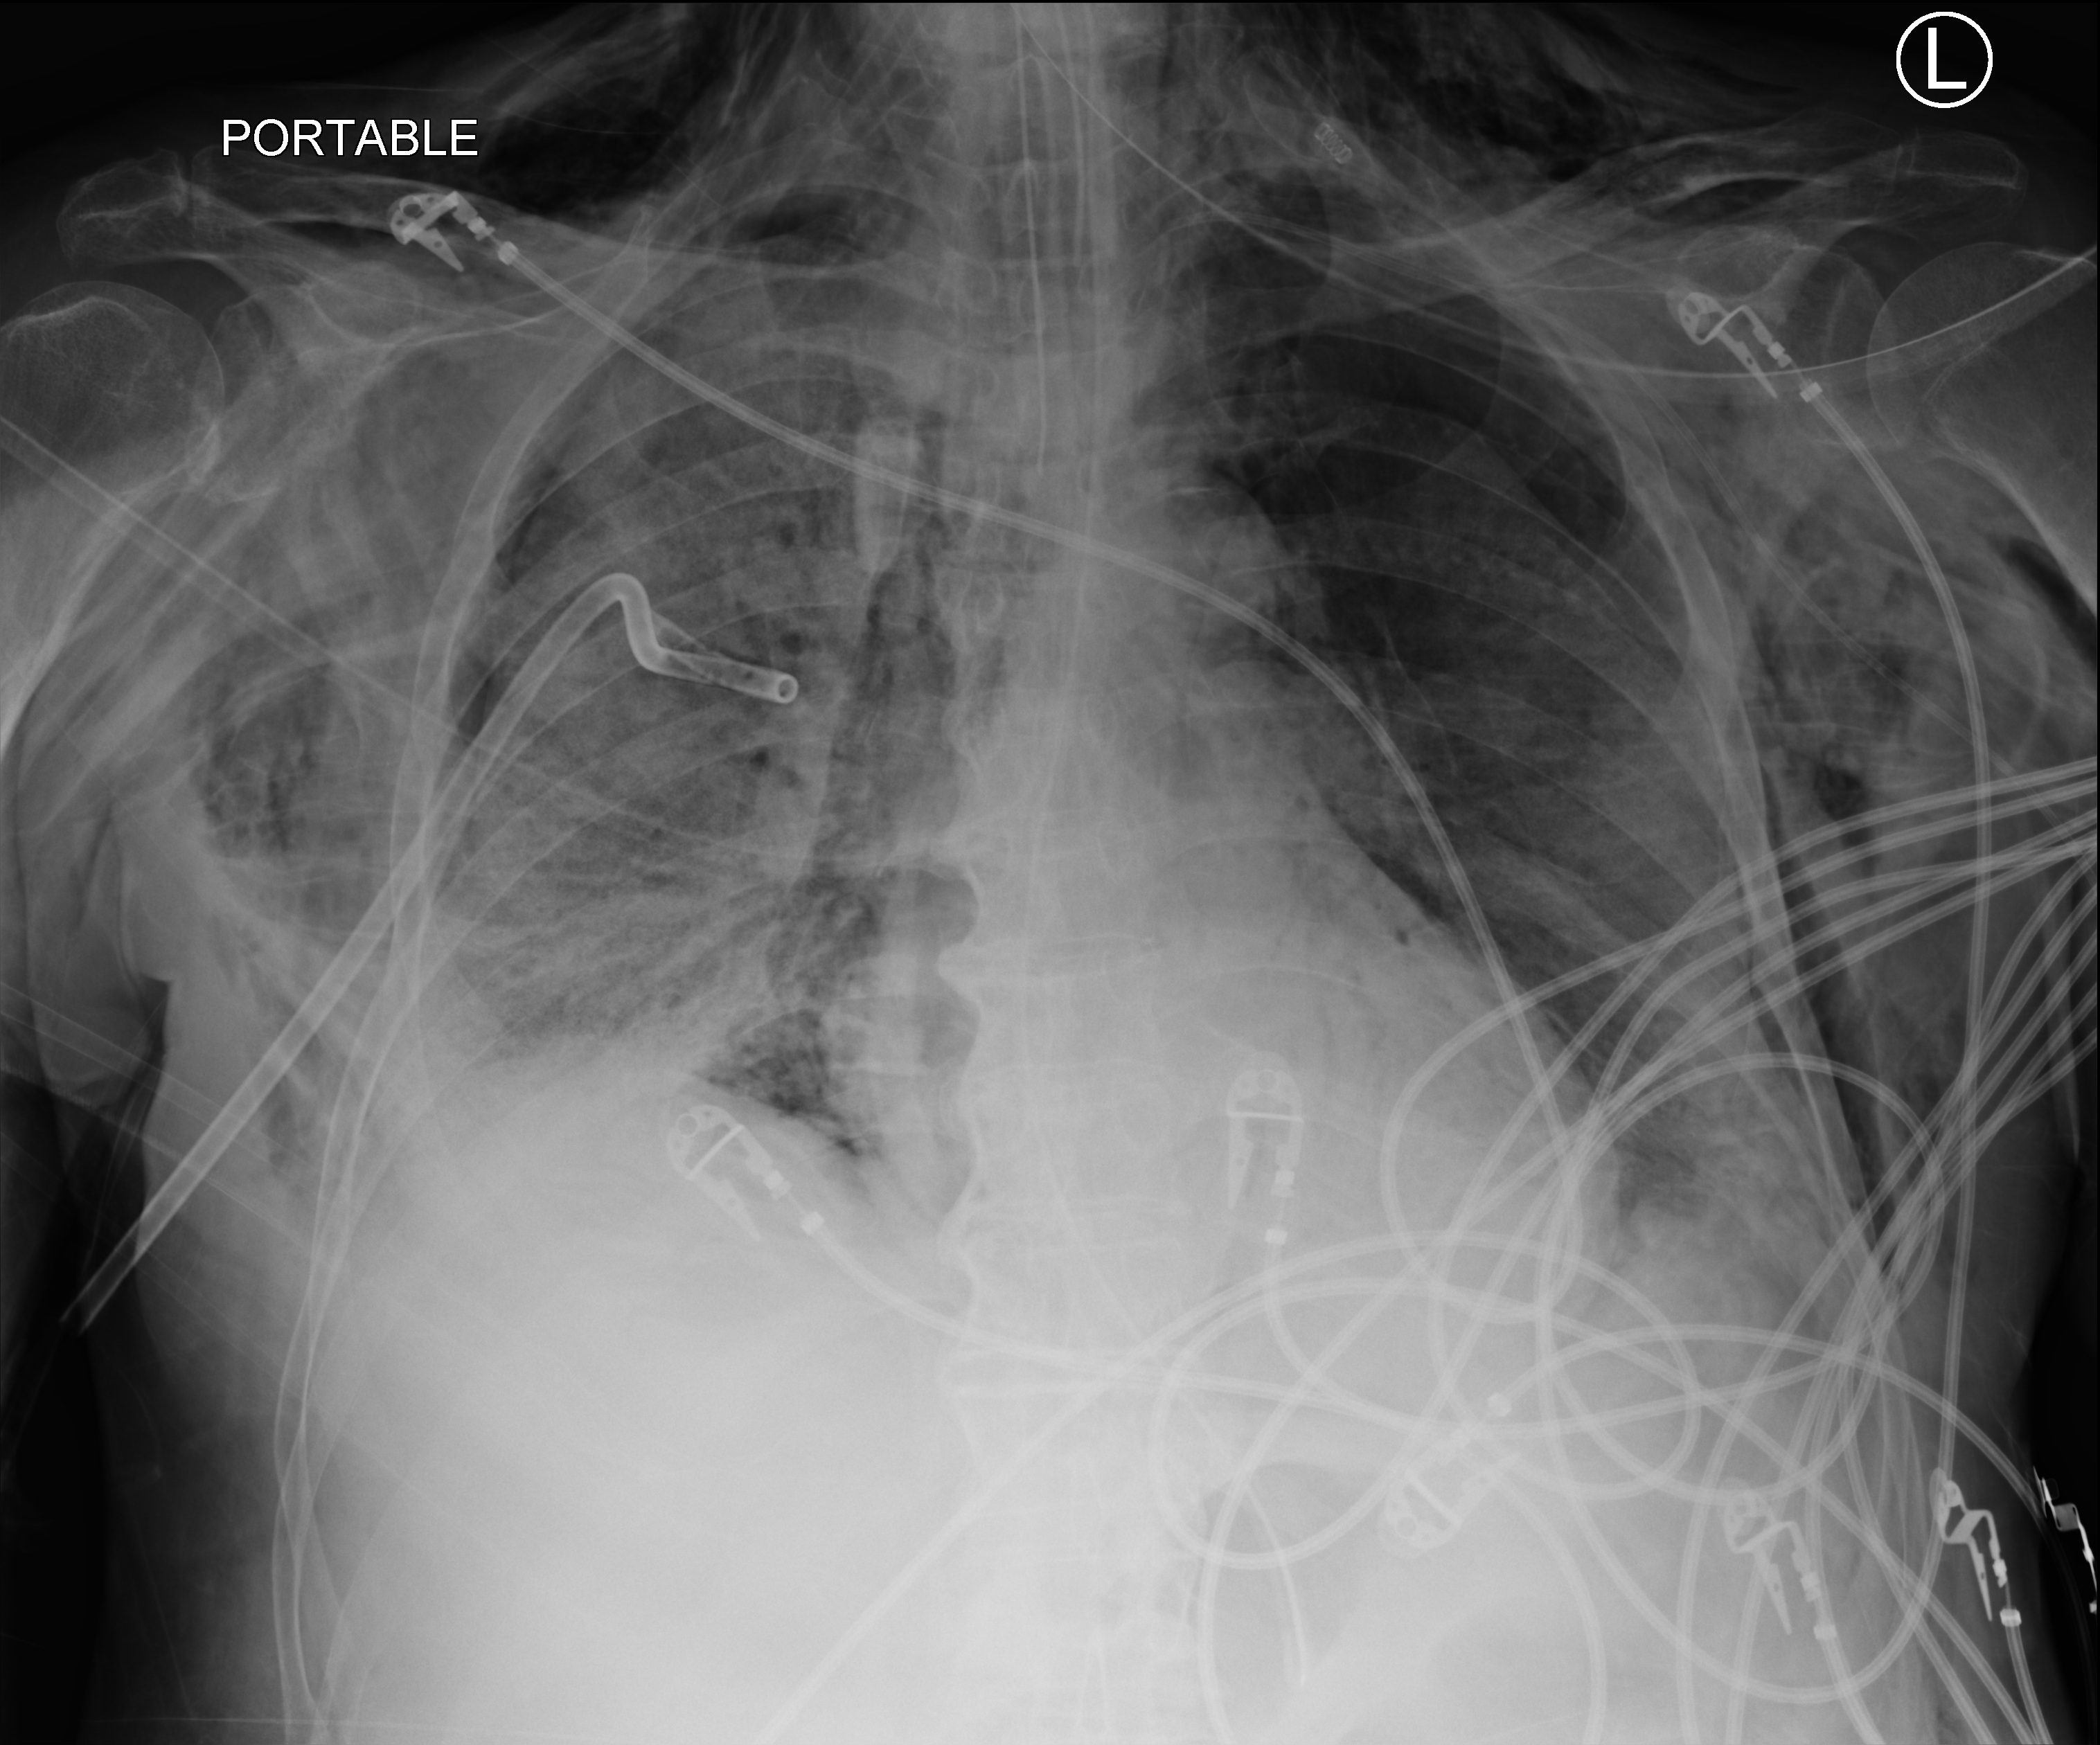
Bedside chest radiograph (computed radiography), anteroposterior (AP) projection. Patient hospitalised with COVID-19; male, aged 75–90 years.
Admission-level facts for this patient (not findings on this image; timing relative to this image not recorded): smoking status (admission record): never; length of hospital stay: 30 days; admitted to intensive care during this hospital stay: yes.